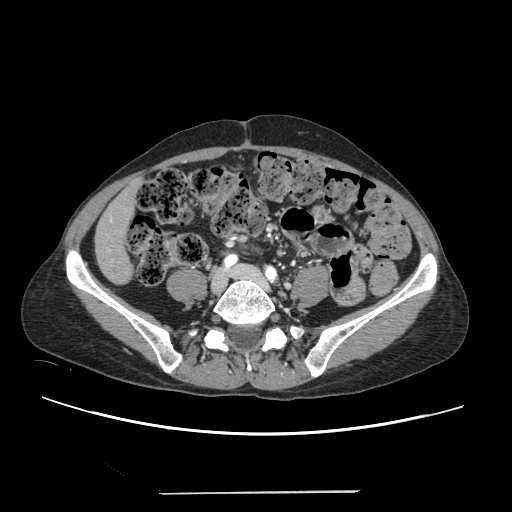
Contrast-enhanced abdominal CT, one axial slice; slice 24 of 240 in the series (ordered by position); soft-tissue window (W 400 / L 40 HU); 512 × 512 image matrix, field of view 371 × 371 mm. Female patient, age 60 years. Case-level facts recorded for this patient, not image findings: diagnosis: colorectal cancer liver metastases, imaged before liver resection; multiple liver metastases: no; largest metastasis: 1.5 cm; disease in both lobes: no.
Structures marked on this image (manually delineated by an expert):
- liver: bounding box (x1, y1, x2, y2) in pixels: (96, 184, 136, 283)
- planned liver remnant (the part of the liver to remain after resection): (96, 184, 137, 283)
- portal vein (with intrahepatic branches): (109, 218, 112, 251)